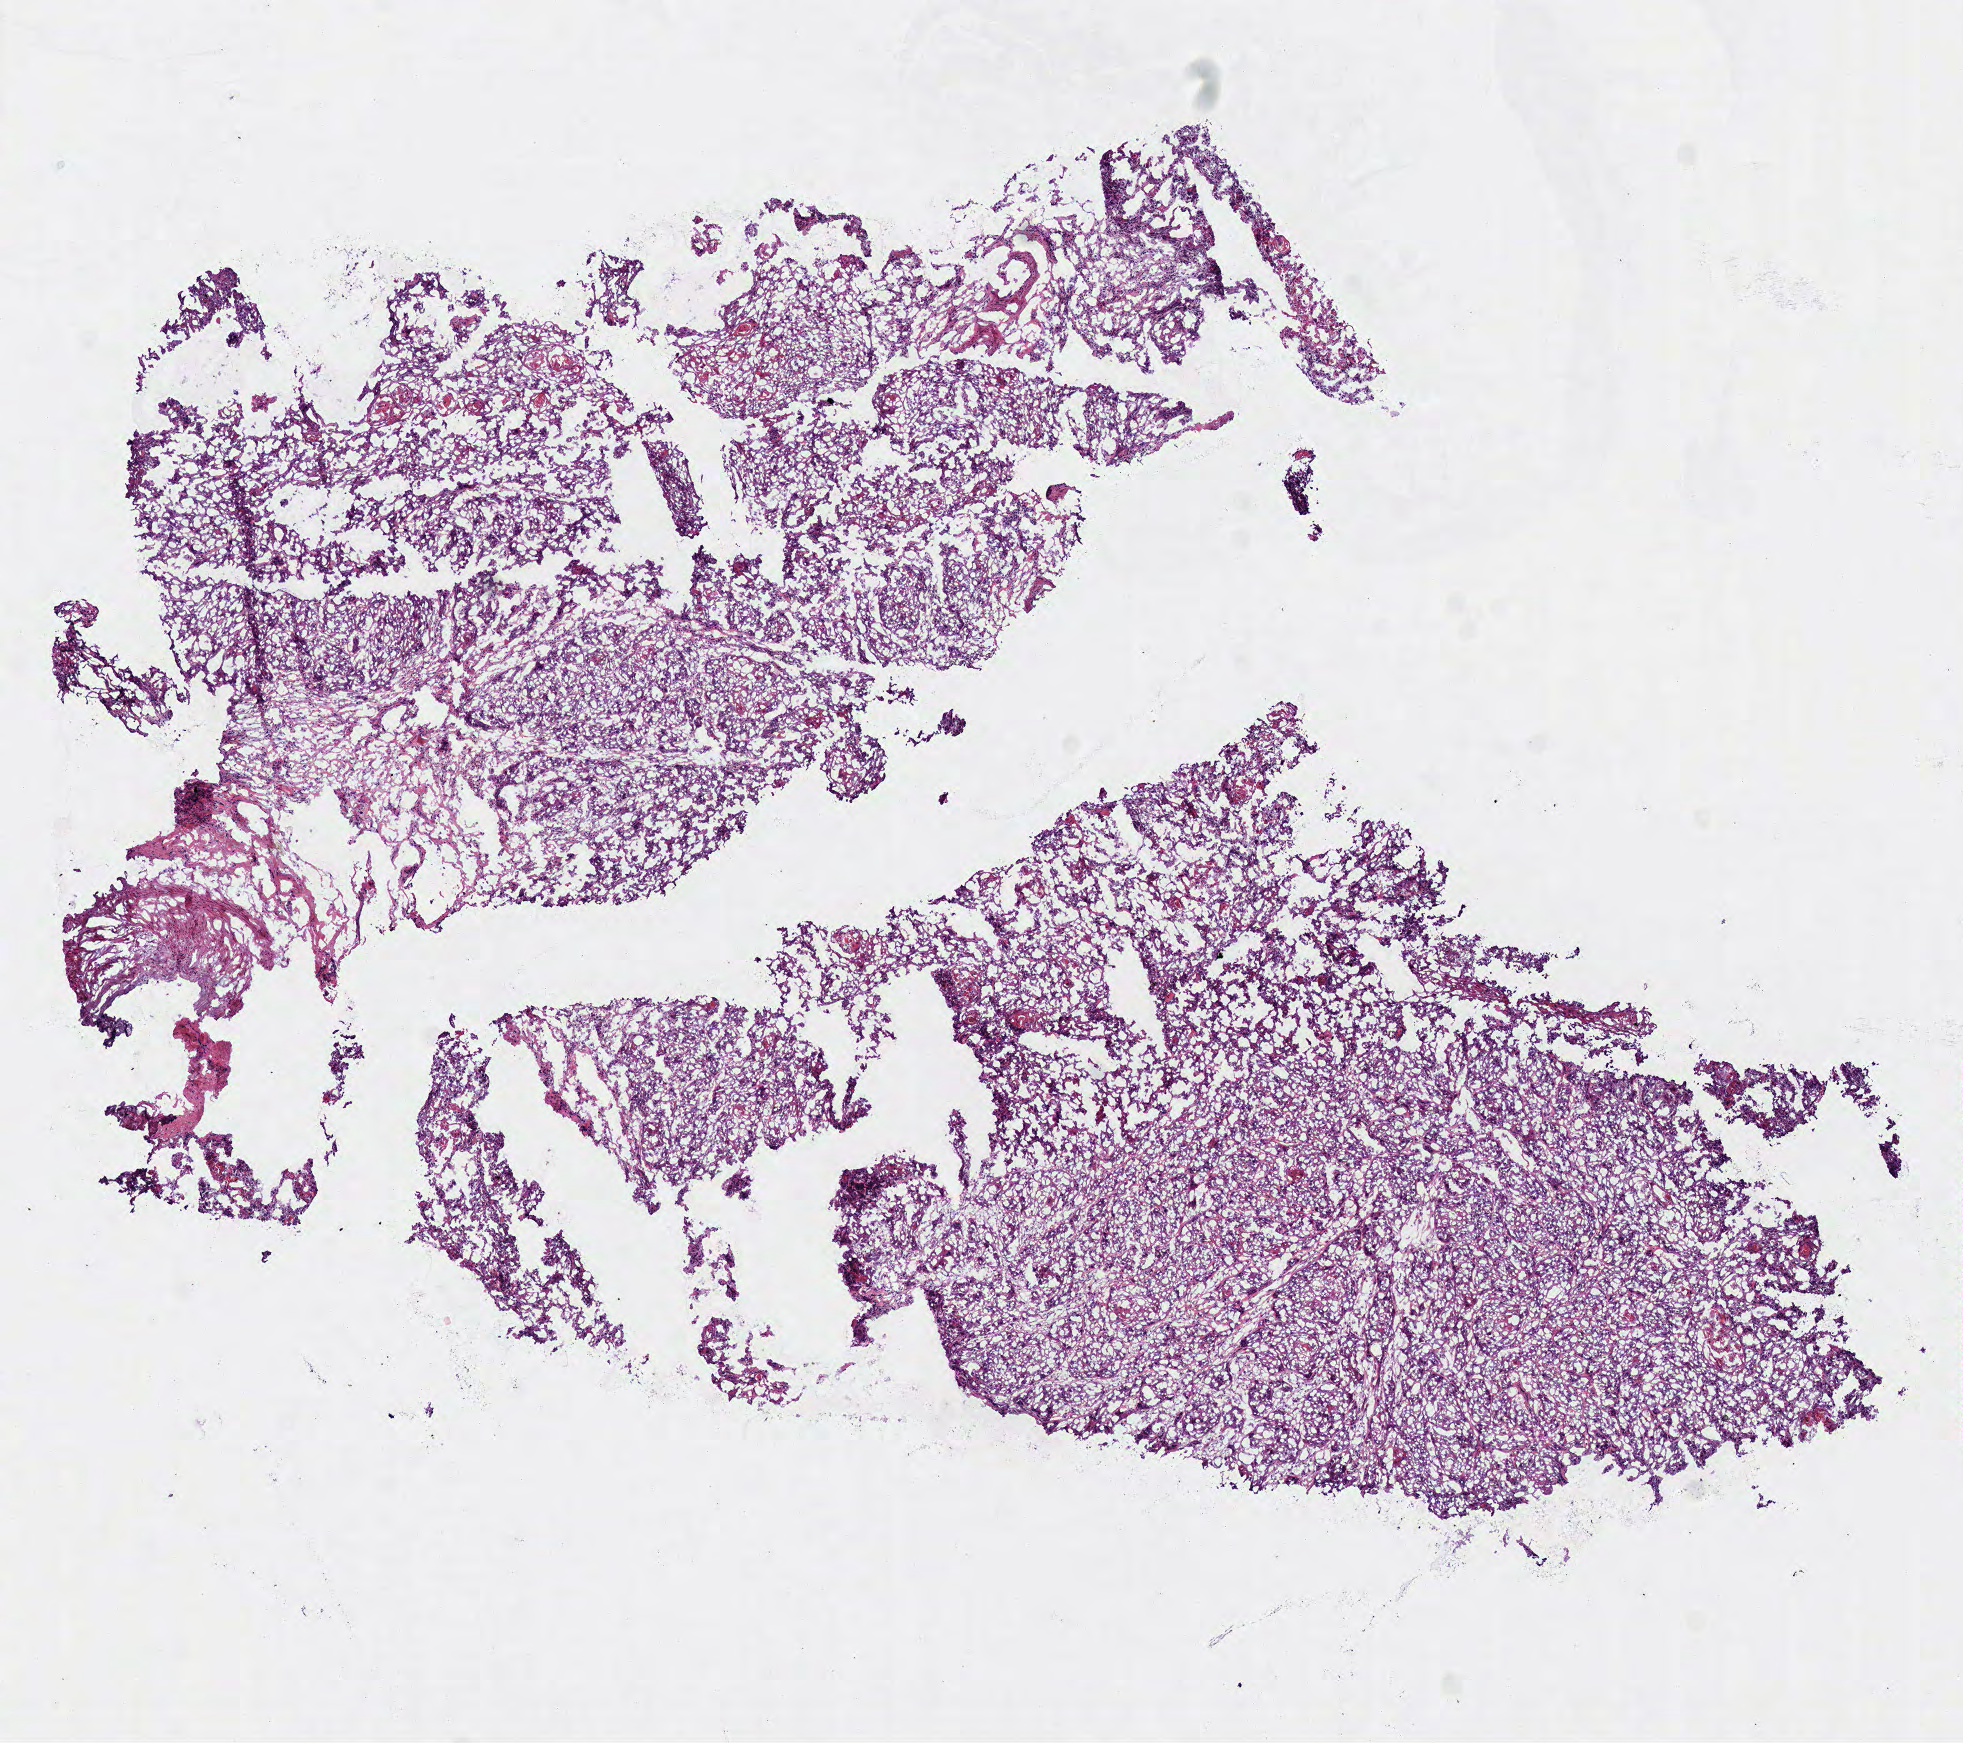
H&E whole-slide image, a low-resolution overview of the entire scanned area, about 7.7 x 6.9 mm (slide scanned at 40x); frozen section from the top of the tissue portion; sample: primary tumour, head and neck. Patient: male, age at initial diagnosis 50 years. Histologic grade: G2 (moderately differentiated). Pathologist review of this section (percent, as recorded): tumour cells 90%, tumour nuclei 85%, normal cells 0%, stromal cells 10%, necrosis 0%.
AJCC pathologic stage: IVA. Diagnosis: Squamous cell carcinoma, NOS (tongue, NOS).